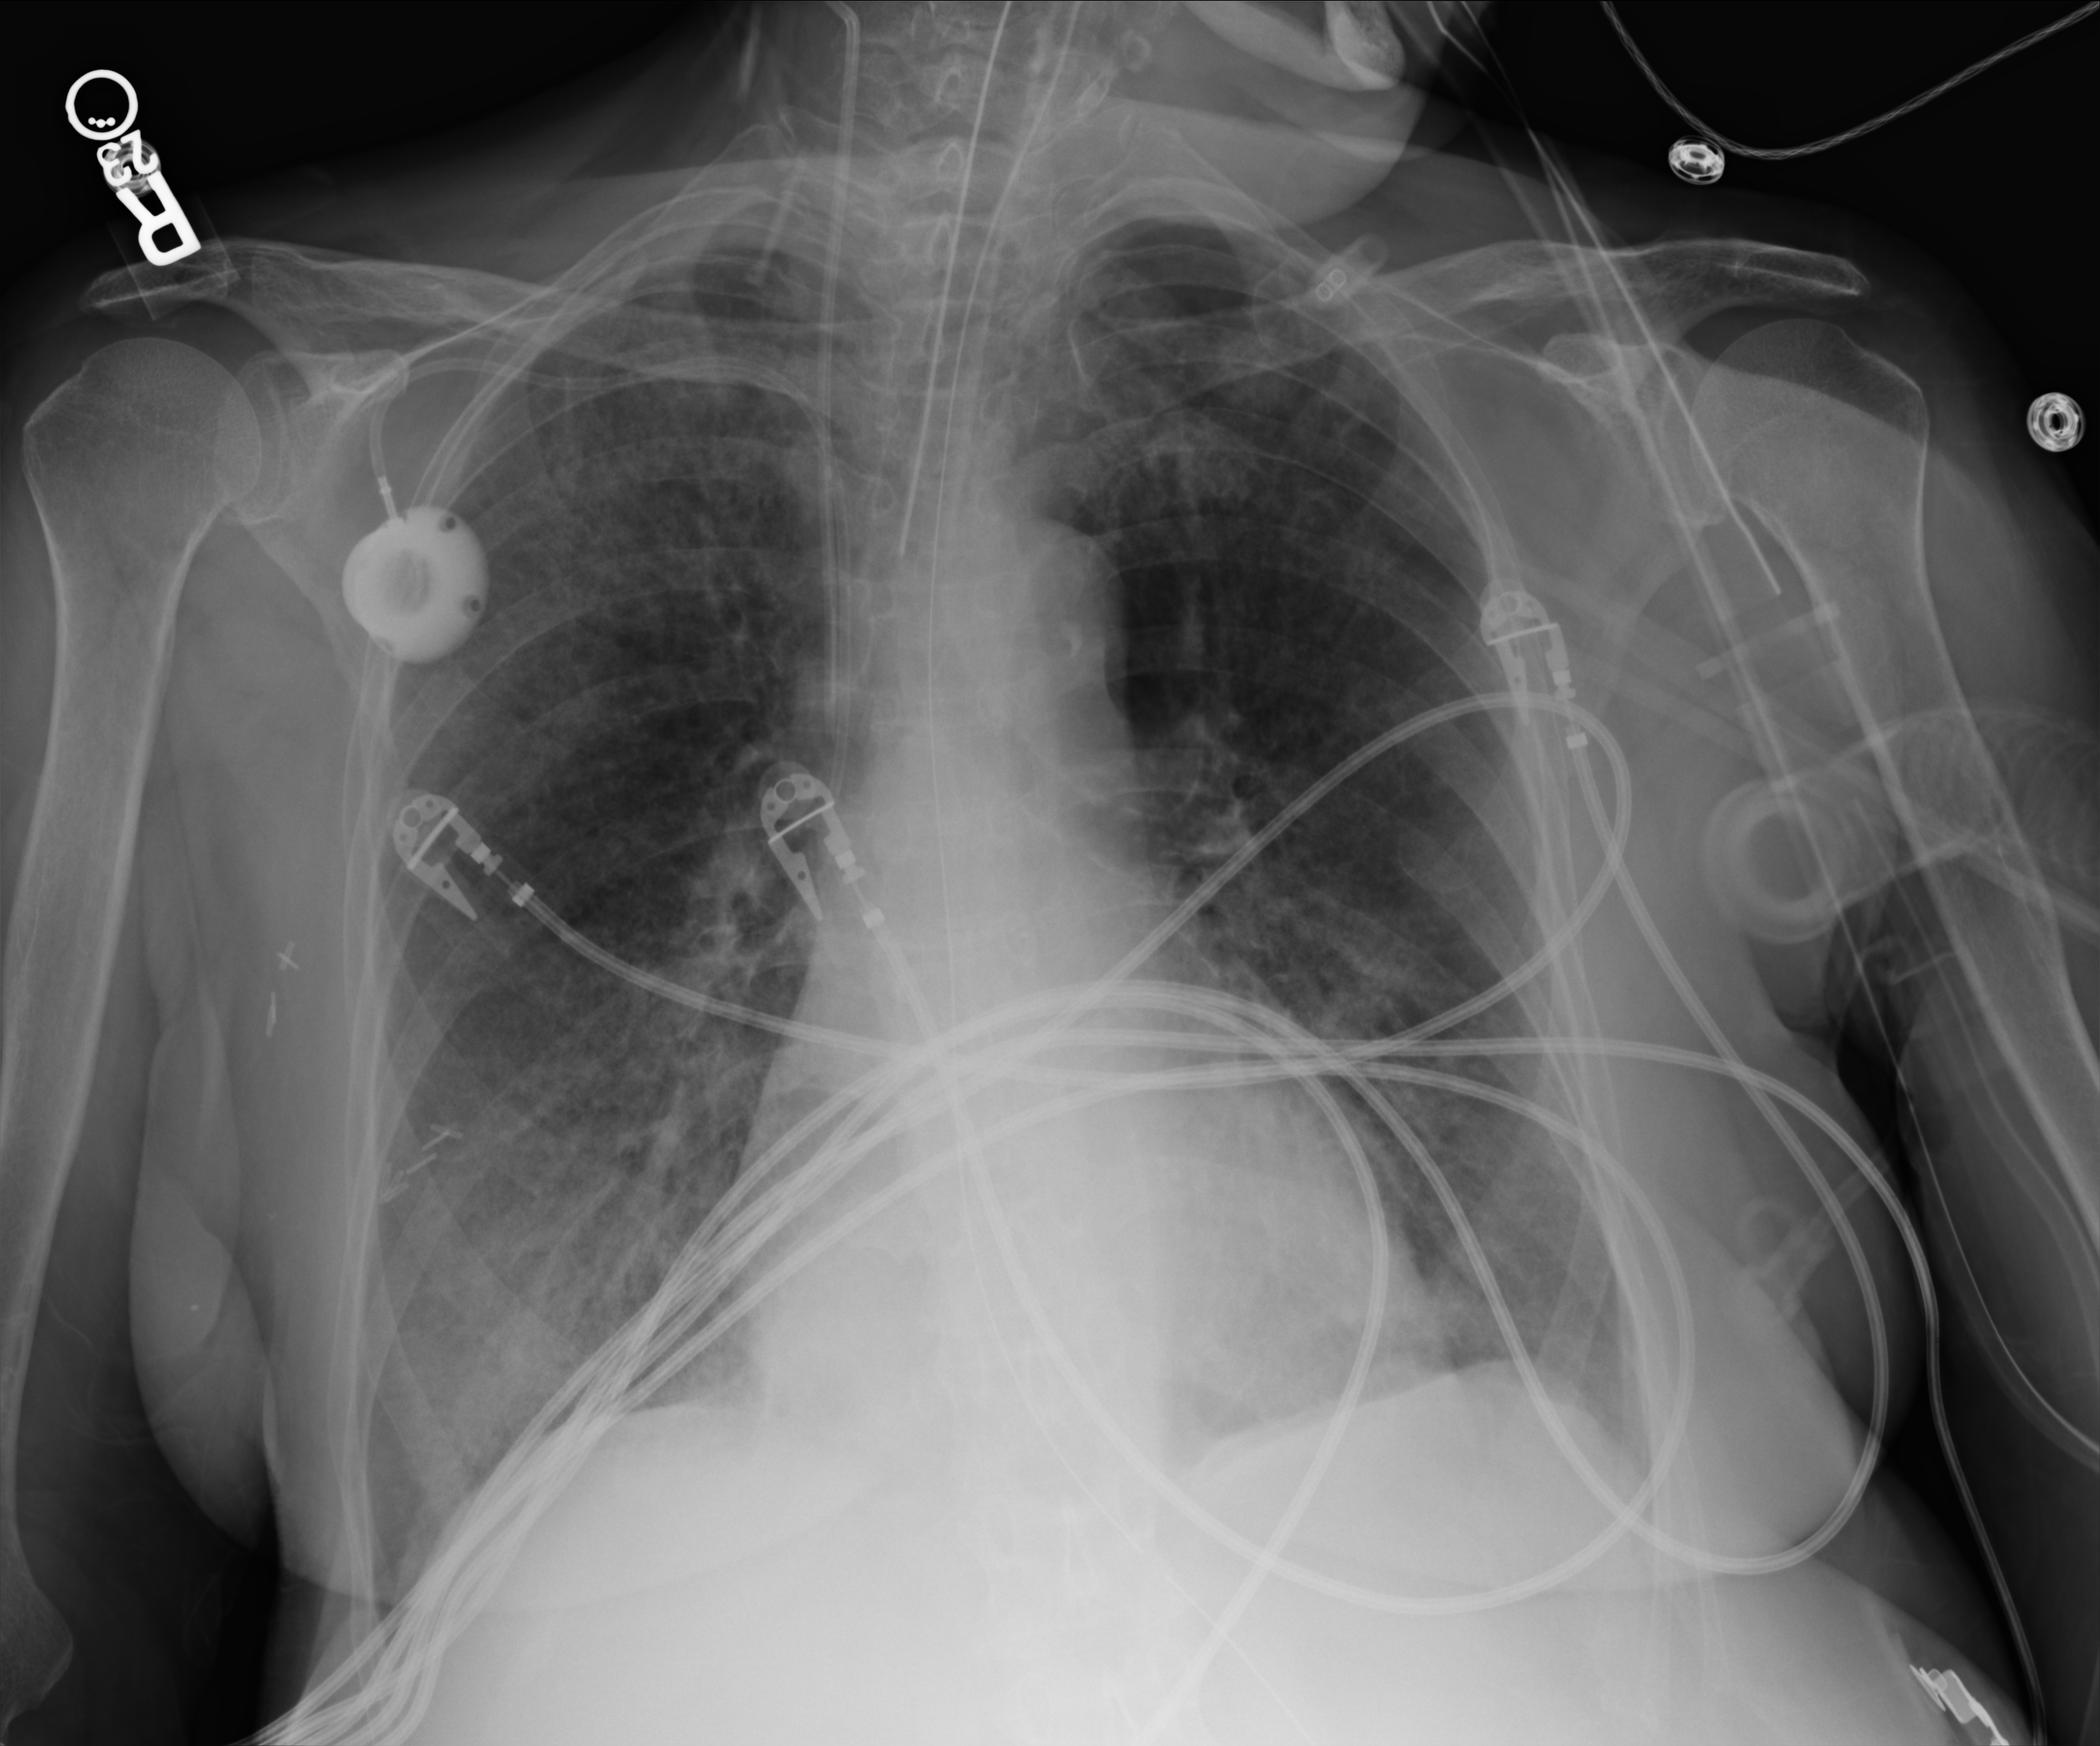
Chest X-ray (portable), anteroposterior (AP) projection. Patient hospitalised with COVID-19; female, aged 60–74 years.
From the hospital-stay record, not from the radiograph (when in the stay this image was taken is not recorded):
- other chronic lung disease (admission record): no
- admitted to intensive care during this hospital stay: yes
- mechanically ventilated during this hospital stay: yes